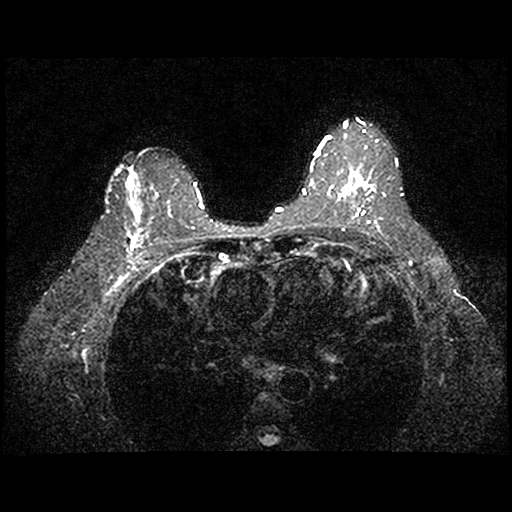
MRI of the breasts; 2 images, each one mid-volume slice chosen by position. Patient in her 50s.
Image 1: axial T2-weighted / STIR image, series "STIR SENSE", slice 46 of 90, 2 mm slice thickness.
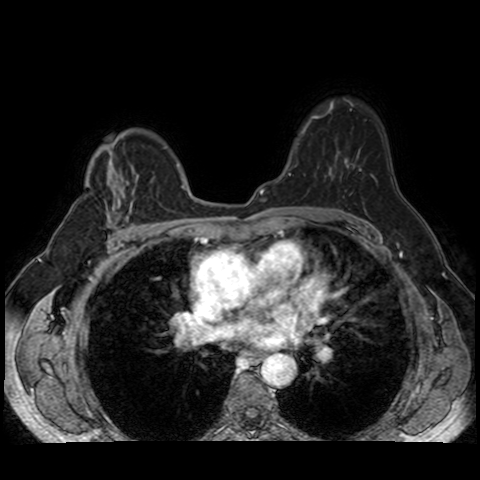
Image 2: axial dynamic contrast-enhanced T1-weighted image, slice 46 of 90, dynamic phase 5 of 8.
MRI impression (as recorded): LEFT BREAST: There is moderate background enhancement. Within the 10:00 position of the mid left breast is an irregularly marginated mass measuring 1.3 x 0.9 x 1.4 cm. The mass has Type III enhancement kinetics with rapid enhancement and rapid washout. No other areas of suspicious enhancement are seen. There is no skin thickening, nipple inversion, or left axillary lymphadenopathy present.
RIGHT BREAST: There is moderate background enhancement. No foci of suspicious enhancement, masses, or areas of architectural distortion seen within the right breast. There is no skin thickening, nipple inversion, or right axillary lymphadenopathy present. IMPRESSION:
1. 1.4 cm enhancing mass at the 10:00 position of the central left breast consistent with biopsy proven breast cancer. No satellite lesions are detected.
2. No evidence of abnormal lymph nodes in either axilla.
3. No evidence of malignancy in the right breast; BI-RADS 6.
Patient-level pathology facts (from the clinical record, not from the images): pathology diagnosis: INVASIVE DUCTAL CARCINOMA MODIFIED SCARFF-BLOOM-RICHARDSON GRADE: III/III. NO IN SITU CARCINOMA PRESENT (left breast); receptor status (as recorded): ER pos (weak), PR pos (weak), HER2 neg; Ki-67 (as recorded): pos (high prolif rate); clinical background (as recorded): 50s y. o. with history of right breast cancer s/p BCT now with newly diagnosed left breast cancer. LMP unknown.